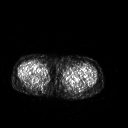
FDG PET of an extremity soft-tissue mass (from a PET/CT study), one axial slice. Position 225 of 267 along the scan axis. 3.27 mm slice thickness. 128 × 128 image matrix, field of view 500 × 500 mm. Patient: female, 42 years. Case-level facts recorded for this patient, not image findings: histological type: pleiomorphic leiomyosarcoma; grade: intermediate; site of the primary tumour: left thigh.
Structures marked on this image (expert contour drawn on MRI and transferred to this co-registered scan by the dataset authors):
- gross tumour volume including surrounding oedema: bounding box [x1, y1, x2, y2] px = [64, 70, 81, 80]